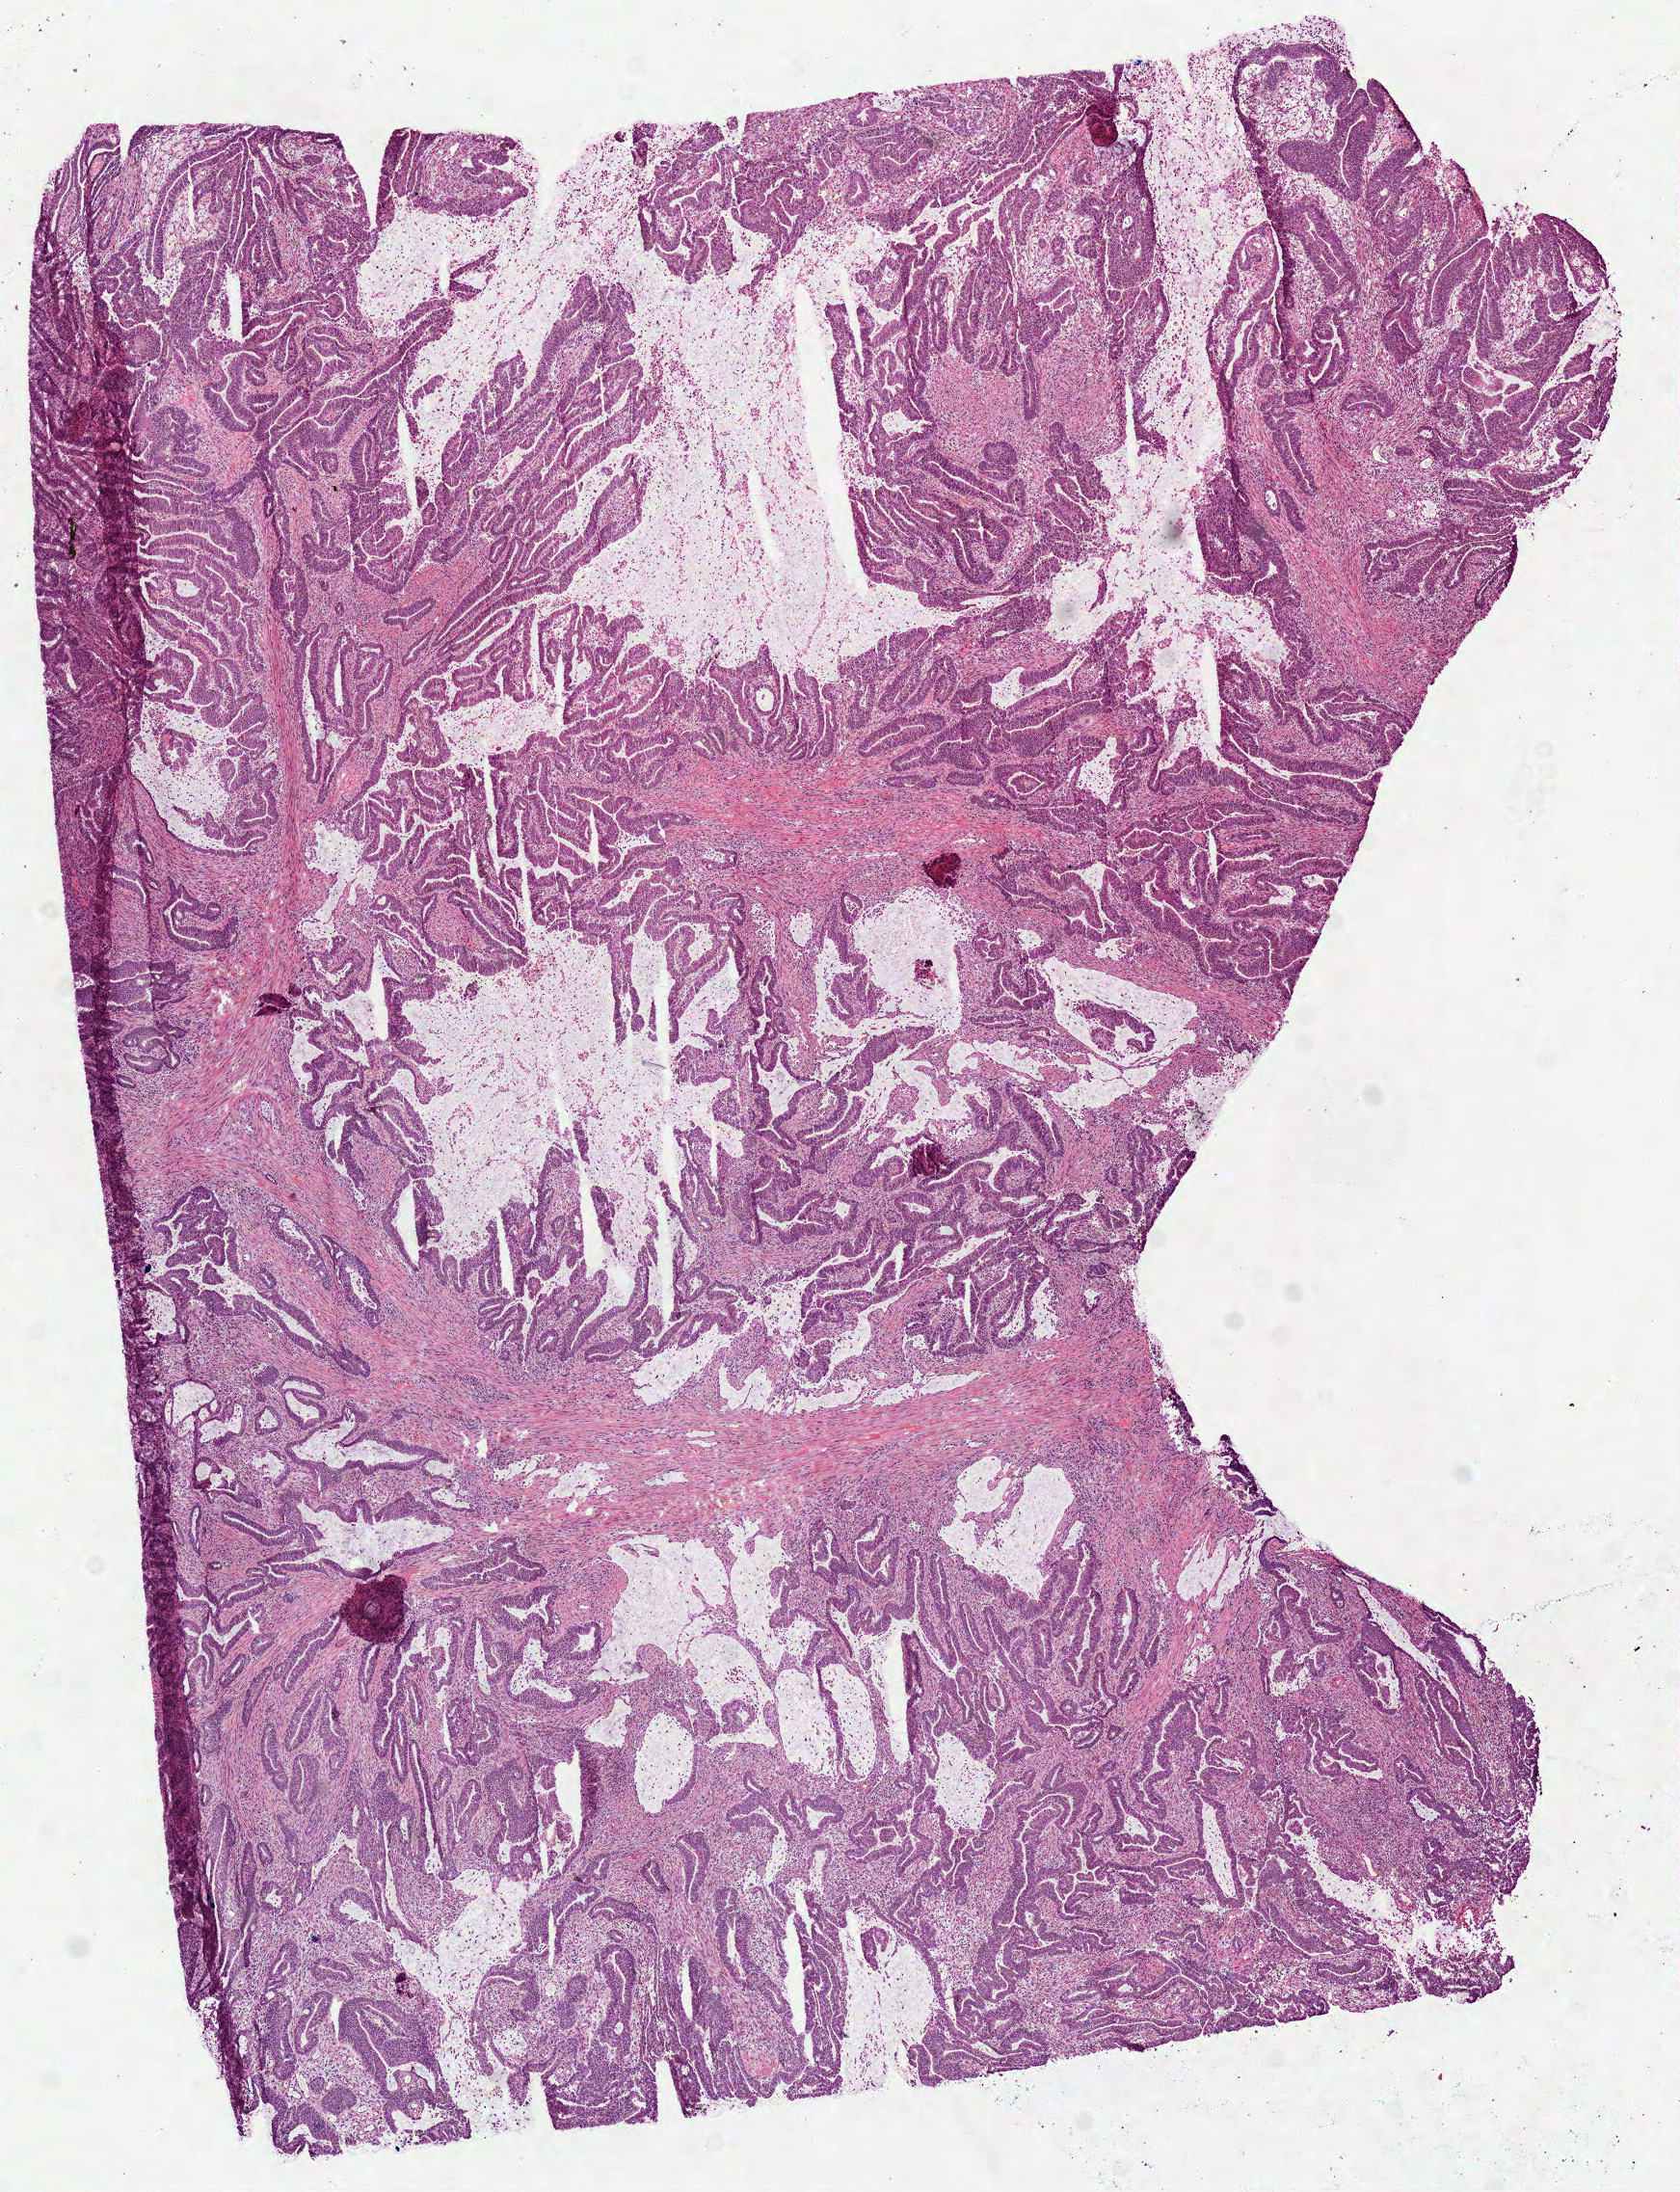
Digitized Hematoxylin and eosin (H&E) stained tissue section (whole slide), whole scanned area (about 7.0 x 9.2 mm) shown as a low-resolution overview; frozen section from the top of the tissue portion; sample: primary tumour, colon. Patient: male, age at initial diagnosis 82 years. Slide review estimates, as recorded: tumour cells 100%, tumour nuclei 80%, normal cells 0%, stromal cells 0%, necrosis 0%. Inflammatory infiltration, as recorded: lymphocyte infiltration 7%, monocyte infiltration 1%, neutrophil infiltration 2%.
AJCC pathologic stage: I (7th edition). Pathologic diagnosis: Adenocarcinoma, NOS.